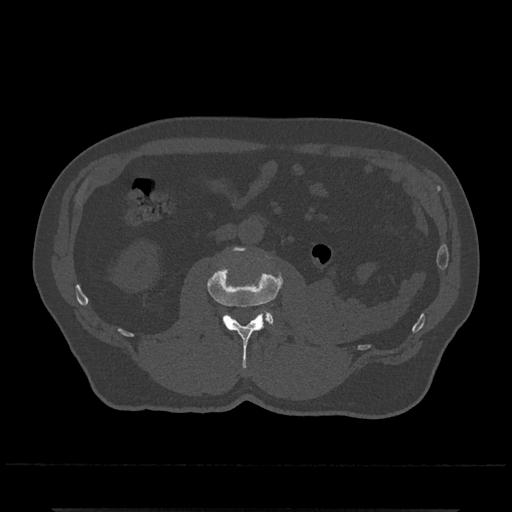
CT including the spine, one axial slice; bone window (W 1800 / L 400 HU); 512 × 512 image matrix, field of view 393 × 393 mm. Male patient, age 67 years. Case-level facts recorded for this patient, not image findings: primary cancer: prostate.
Annotated regions visible in this slice (semi-automatic segmentation, software-assisted and operator-edited):
- L2 vertebra: box from (x=207, y=247) to (x=283, y=368) px
- L3 vertebra: (x=258, y=310)–(x=273, y=326)